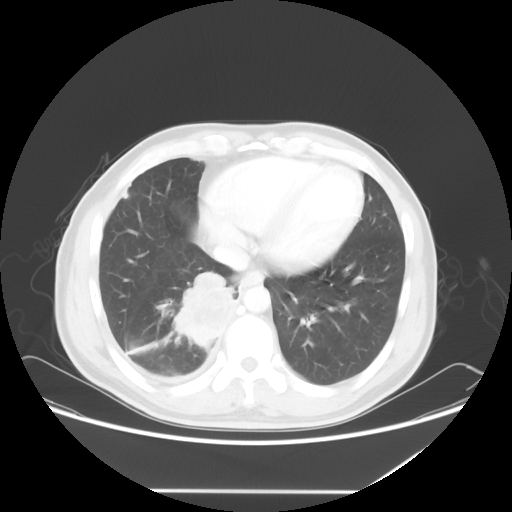
Chest CT, one axial slice; slice 19 of 60 in the series (ordered by position); reconstruction kernel STANDARD; 120 kVp; lung window (W 1500 / L -600 HU); 5 mm slice thickness; 512 × 512 image matrix, field of view 419 × 419 mm. Male patient, age 48 years. From the clinical record (not read from this slice): clinical TNM (as recorded): T3 N3 M1a.
Annotated regions visible in this slice (rectangle marked by the reading radiologist):
- lung tumour (recorded histology: squamous cell carcinoma): bounding box <162,266,240,353> (left, top, right, bottom; pixels)